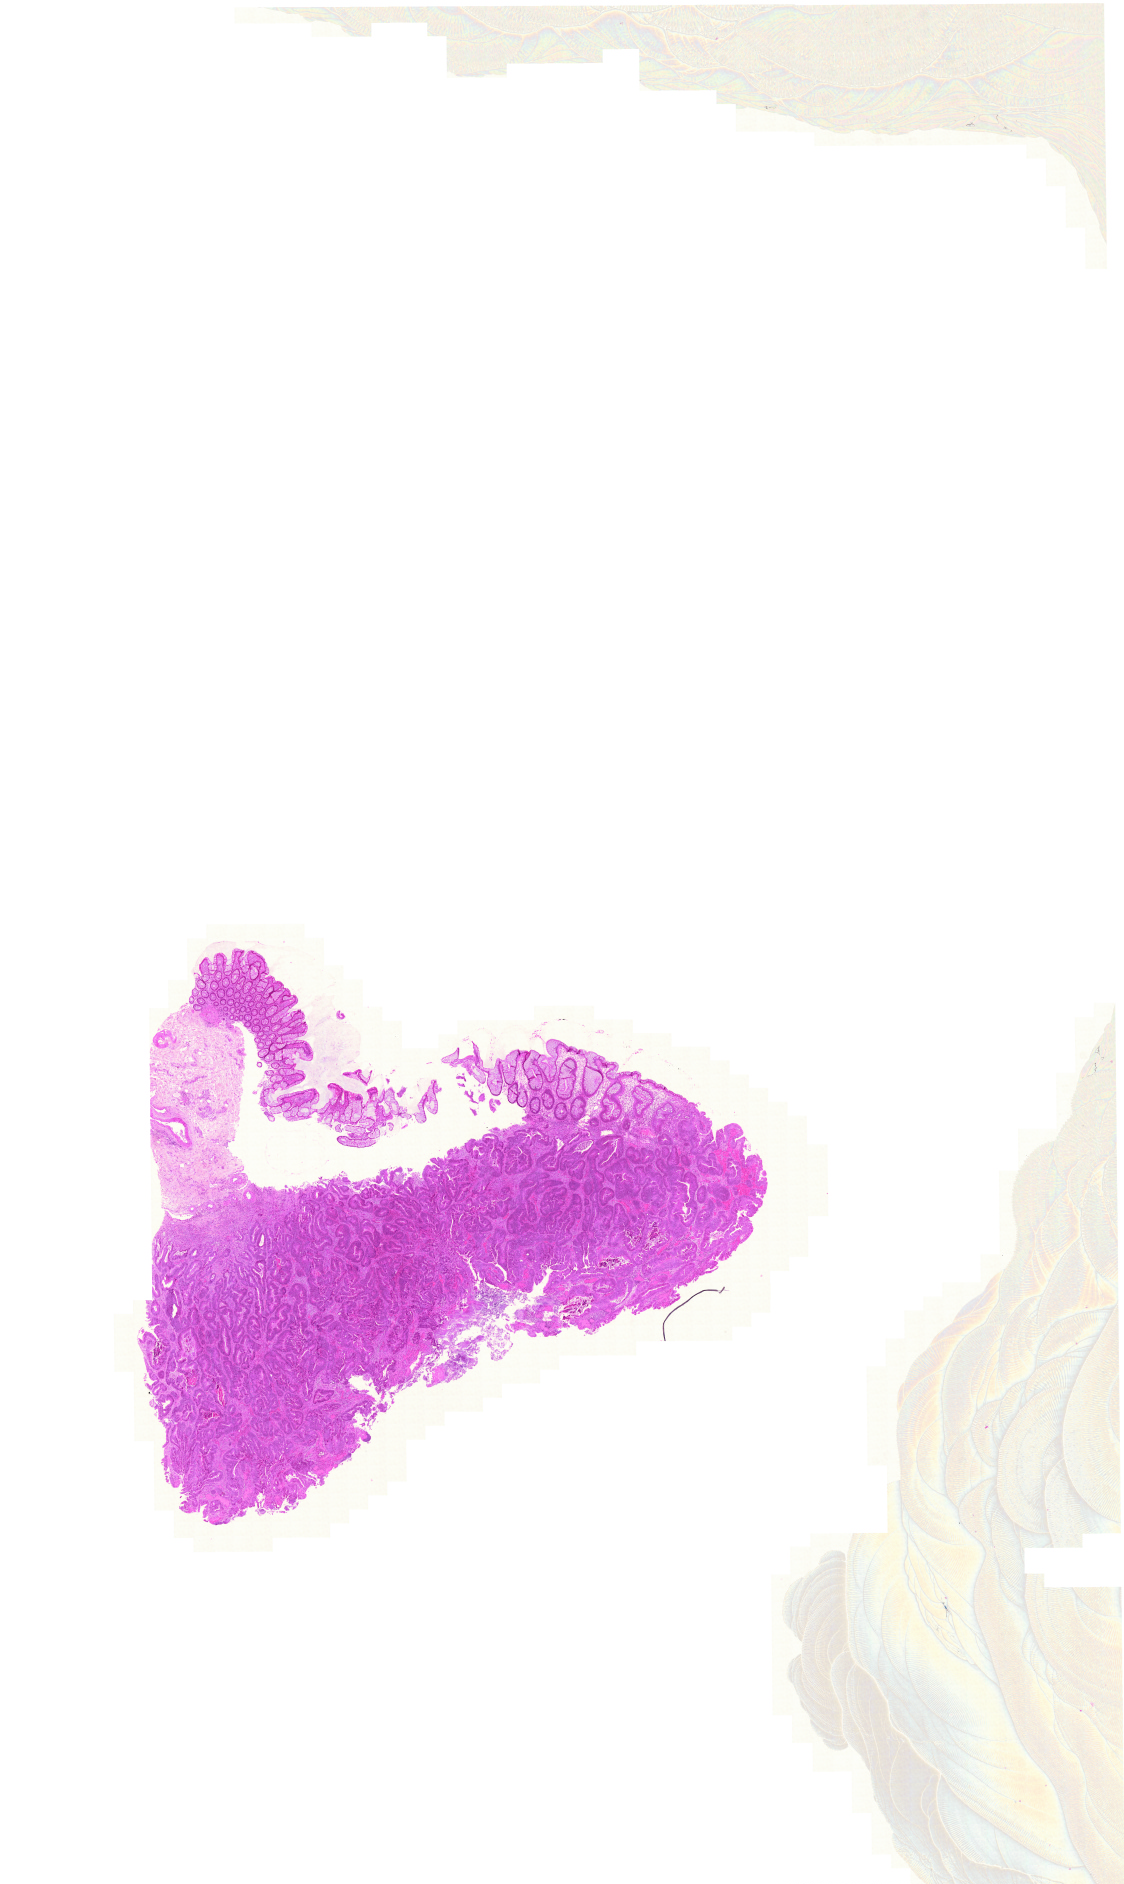
Digitized Hematoxylin and eosin (H&E) stained tissue section (whole slide), a low-resolution overview of the entire scanned area, about 16.7 x 28.0 mm; FFPE section; colon, primary tumour sample. Female patient; age at initial diagnosis 63 years.
• pathologic diagnosis: Adenocarcinoma, NOS
• AJCC pathologic stage: III (5th edition)
• lymph nodes positive (case pathology): 1 of 15 examined